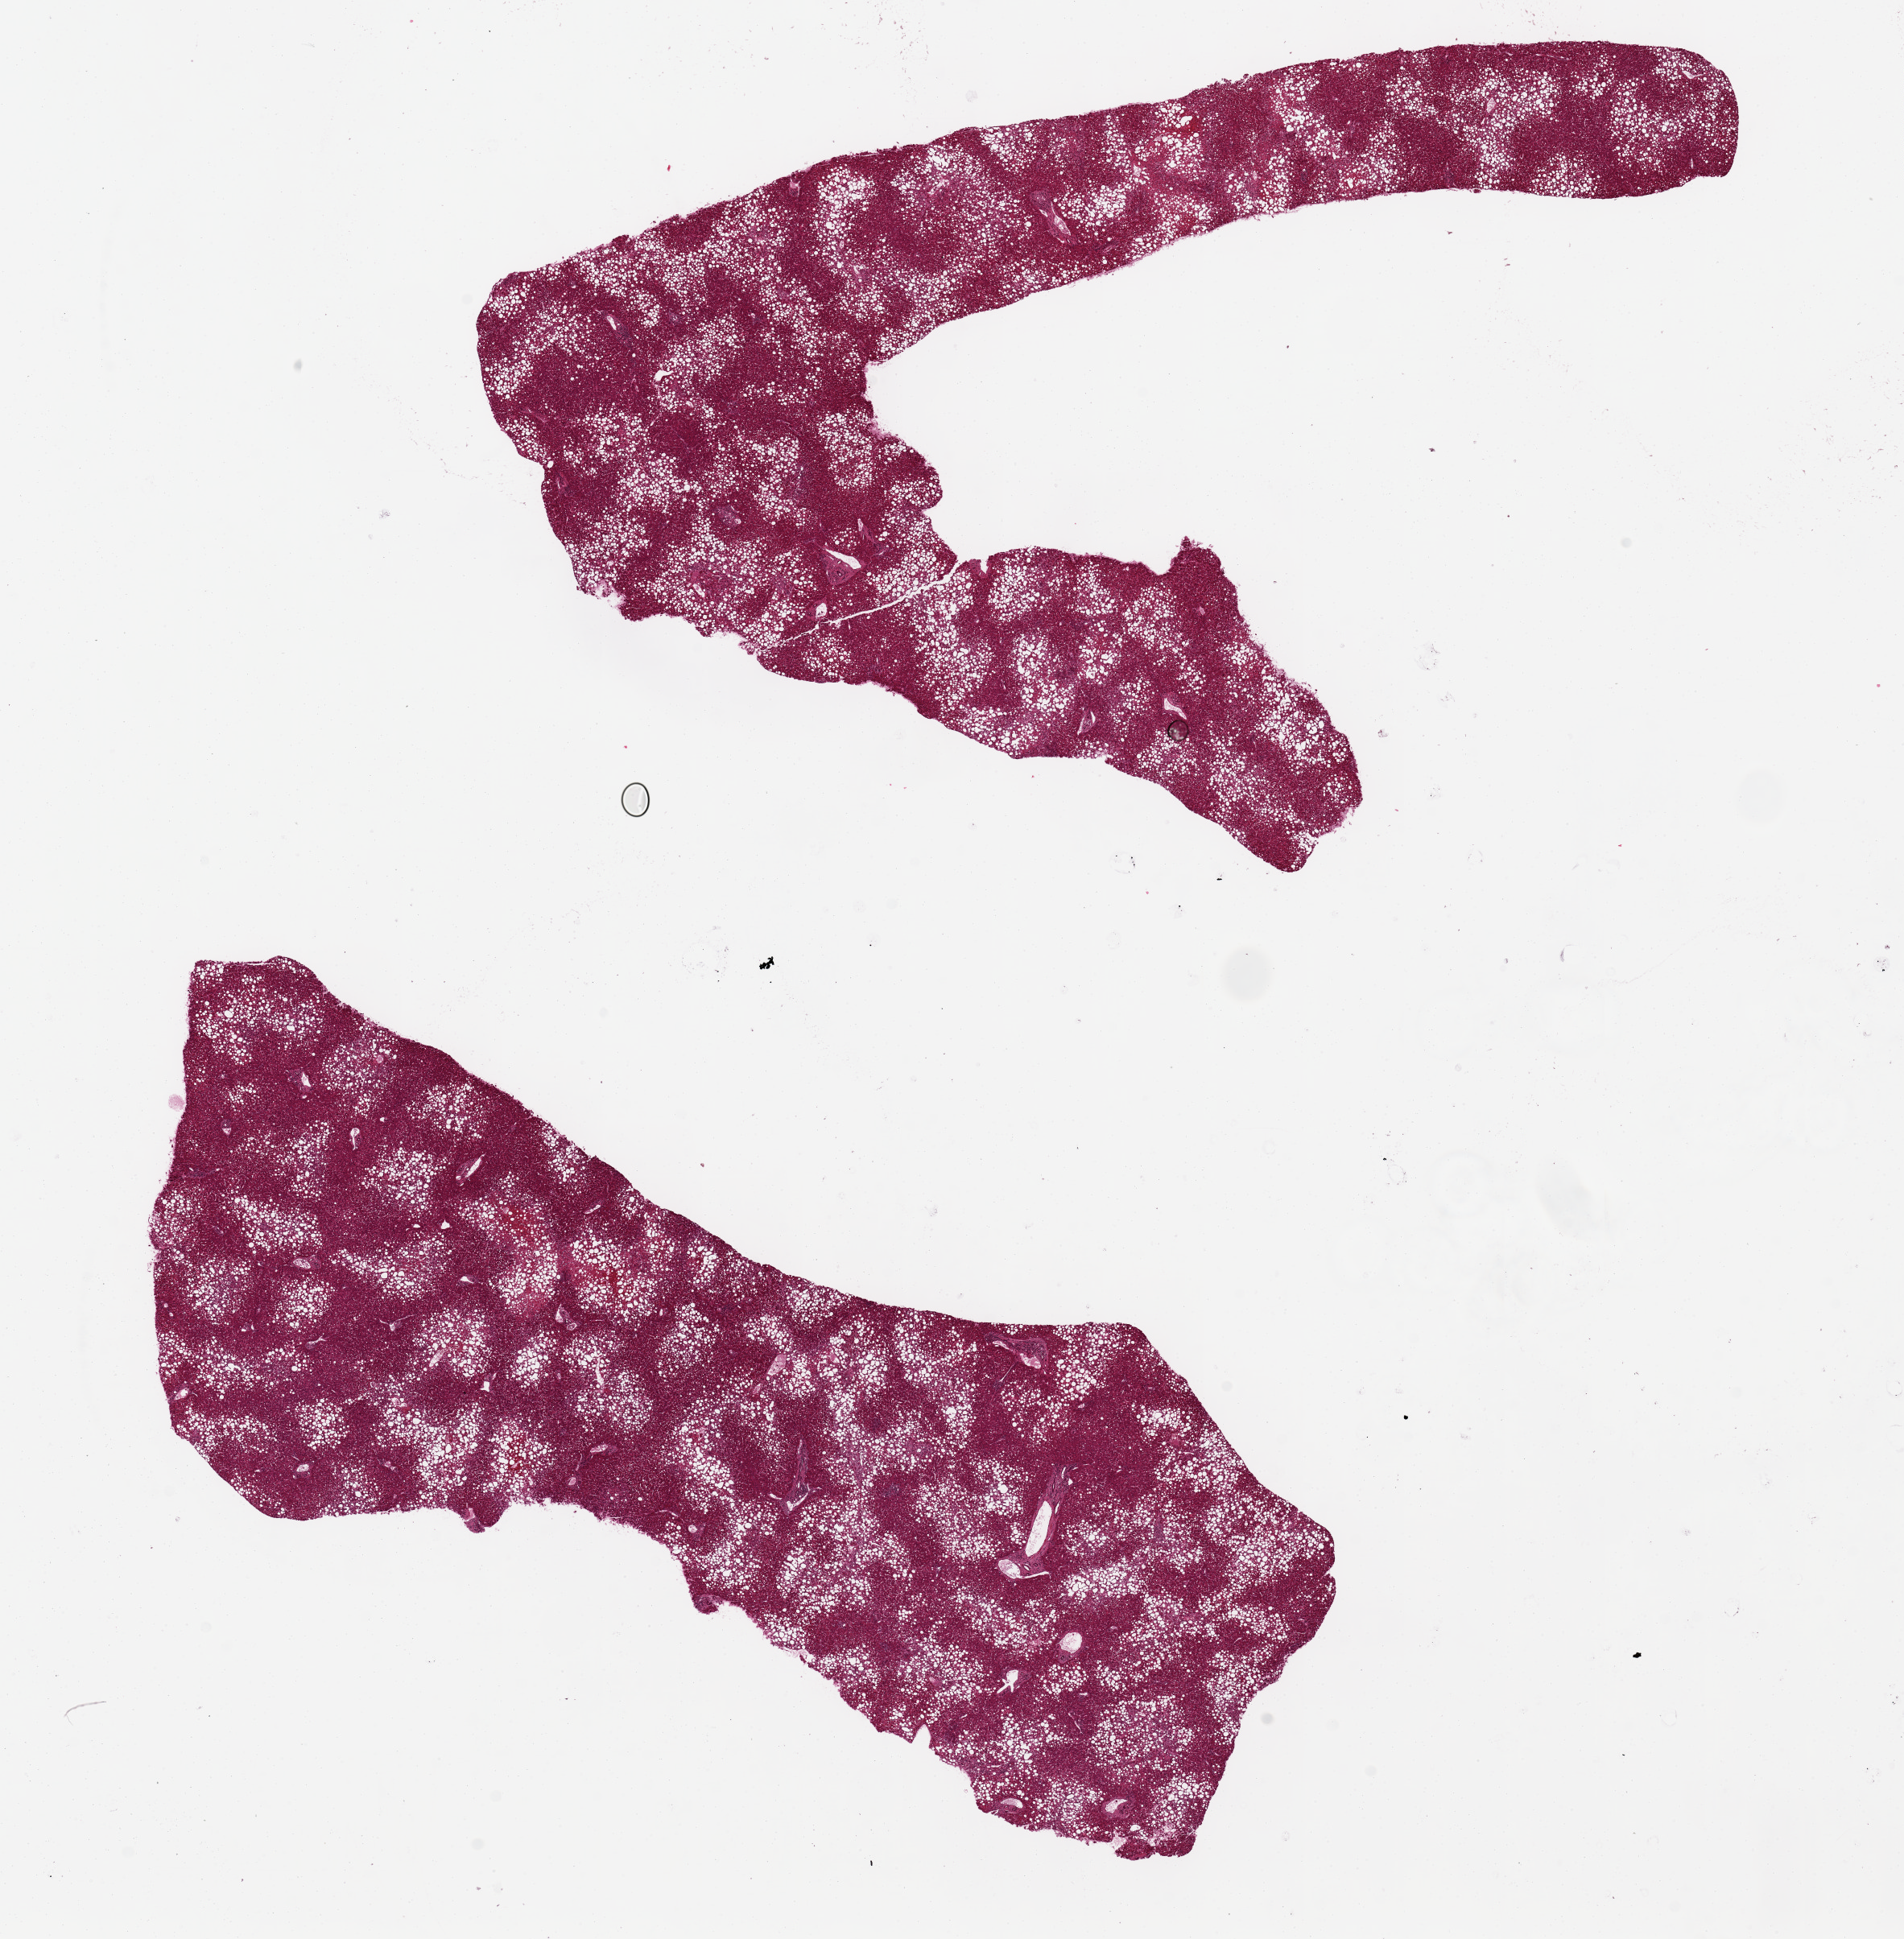
Whole-slide image, hematoxylin and eosin (H&E) stain — shown as a low-resolution overview of the whole scanned area (about 18.7 x 19.1 mm). PAXgene-fixed paraffin-embedded (PFPE) section. Section of liver (target tissue). Donor tissue sample. Male donor.
Reviewer comment on this tissue sample: 2 pieces, 12.5x8 & 13x5mm; severe macrovesicular steatosis.